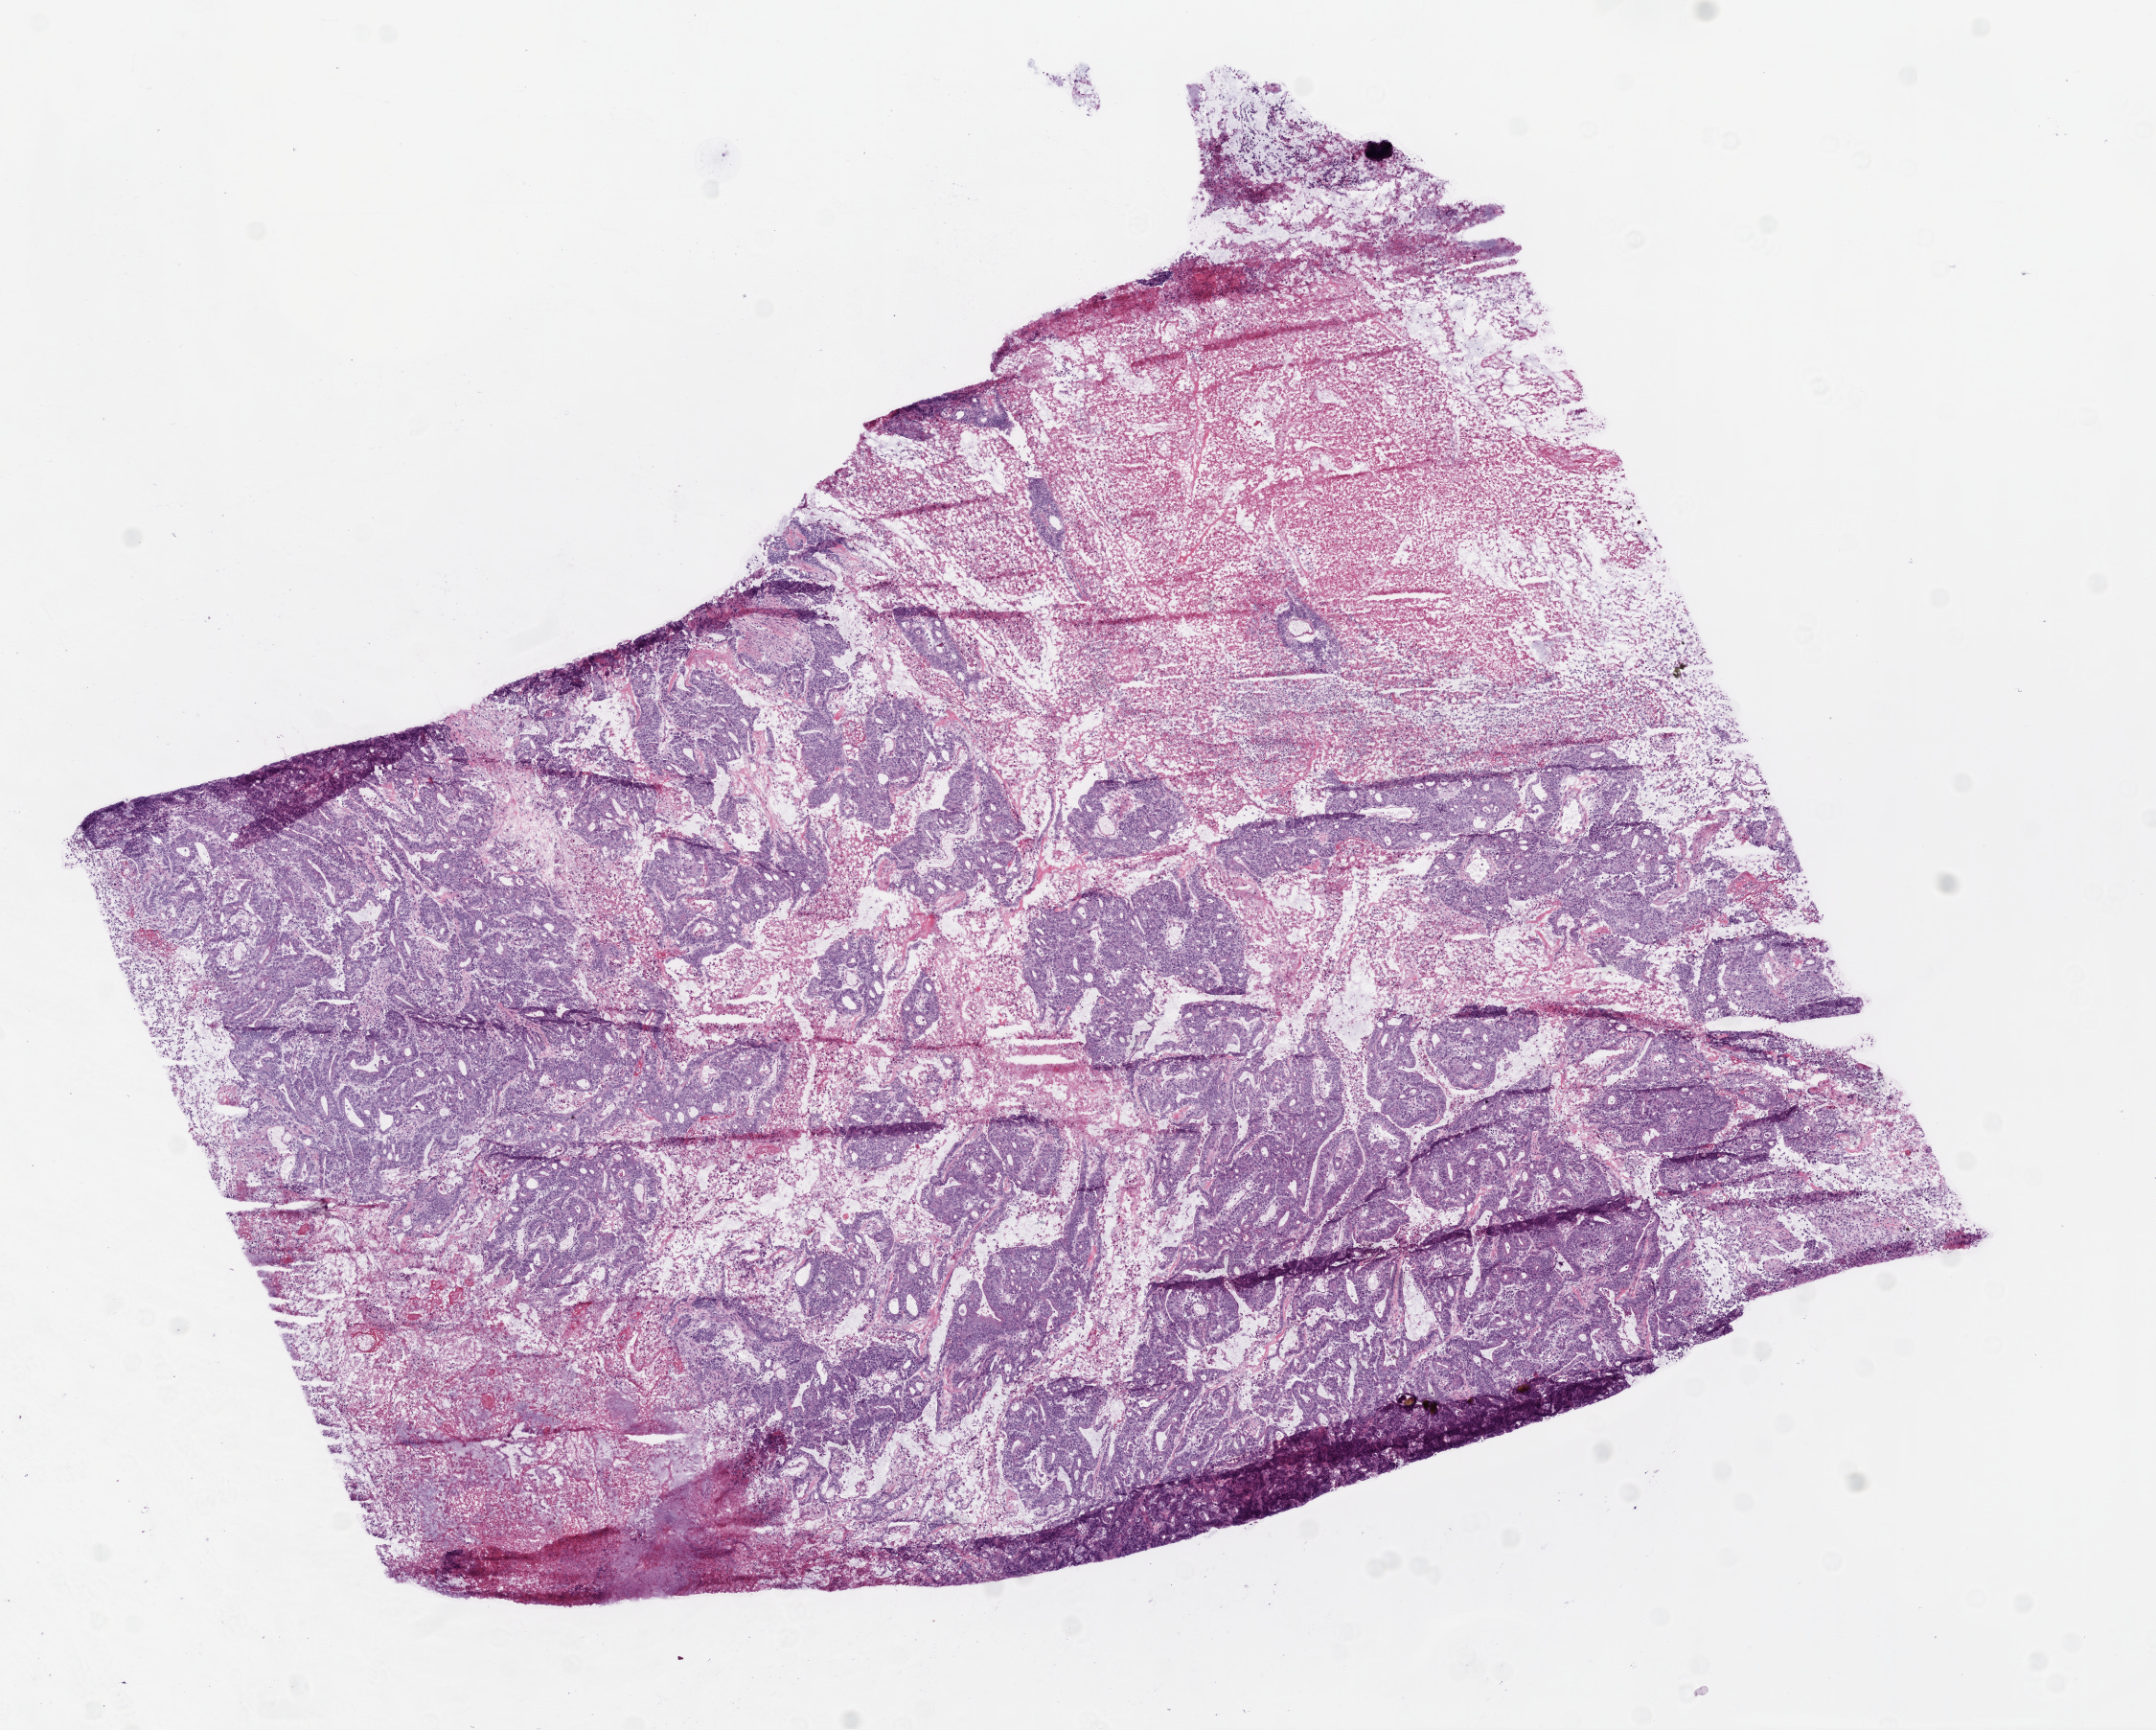
H&E-stained whole-slide image — whole scanned area (about 9.0 x 7.2 mm) shown as a low-resolution overview; frozen section from the bottom of the tissue portion; primary tumour sample from the colon. Patient: female, age at initial diagnosis 71 years. Pathologist review of this section (percent, as recorded): tumour cells 65%, tumour nuclei 80%.
Pathologic diagnosis: Mucinous adenocarcinoma.